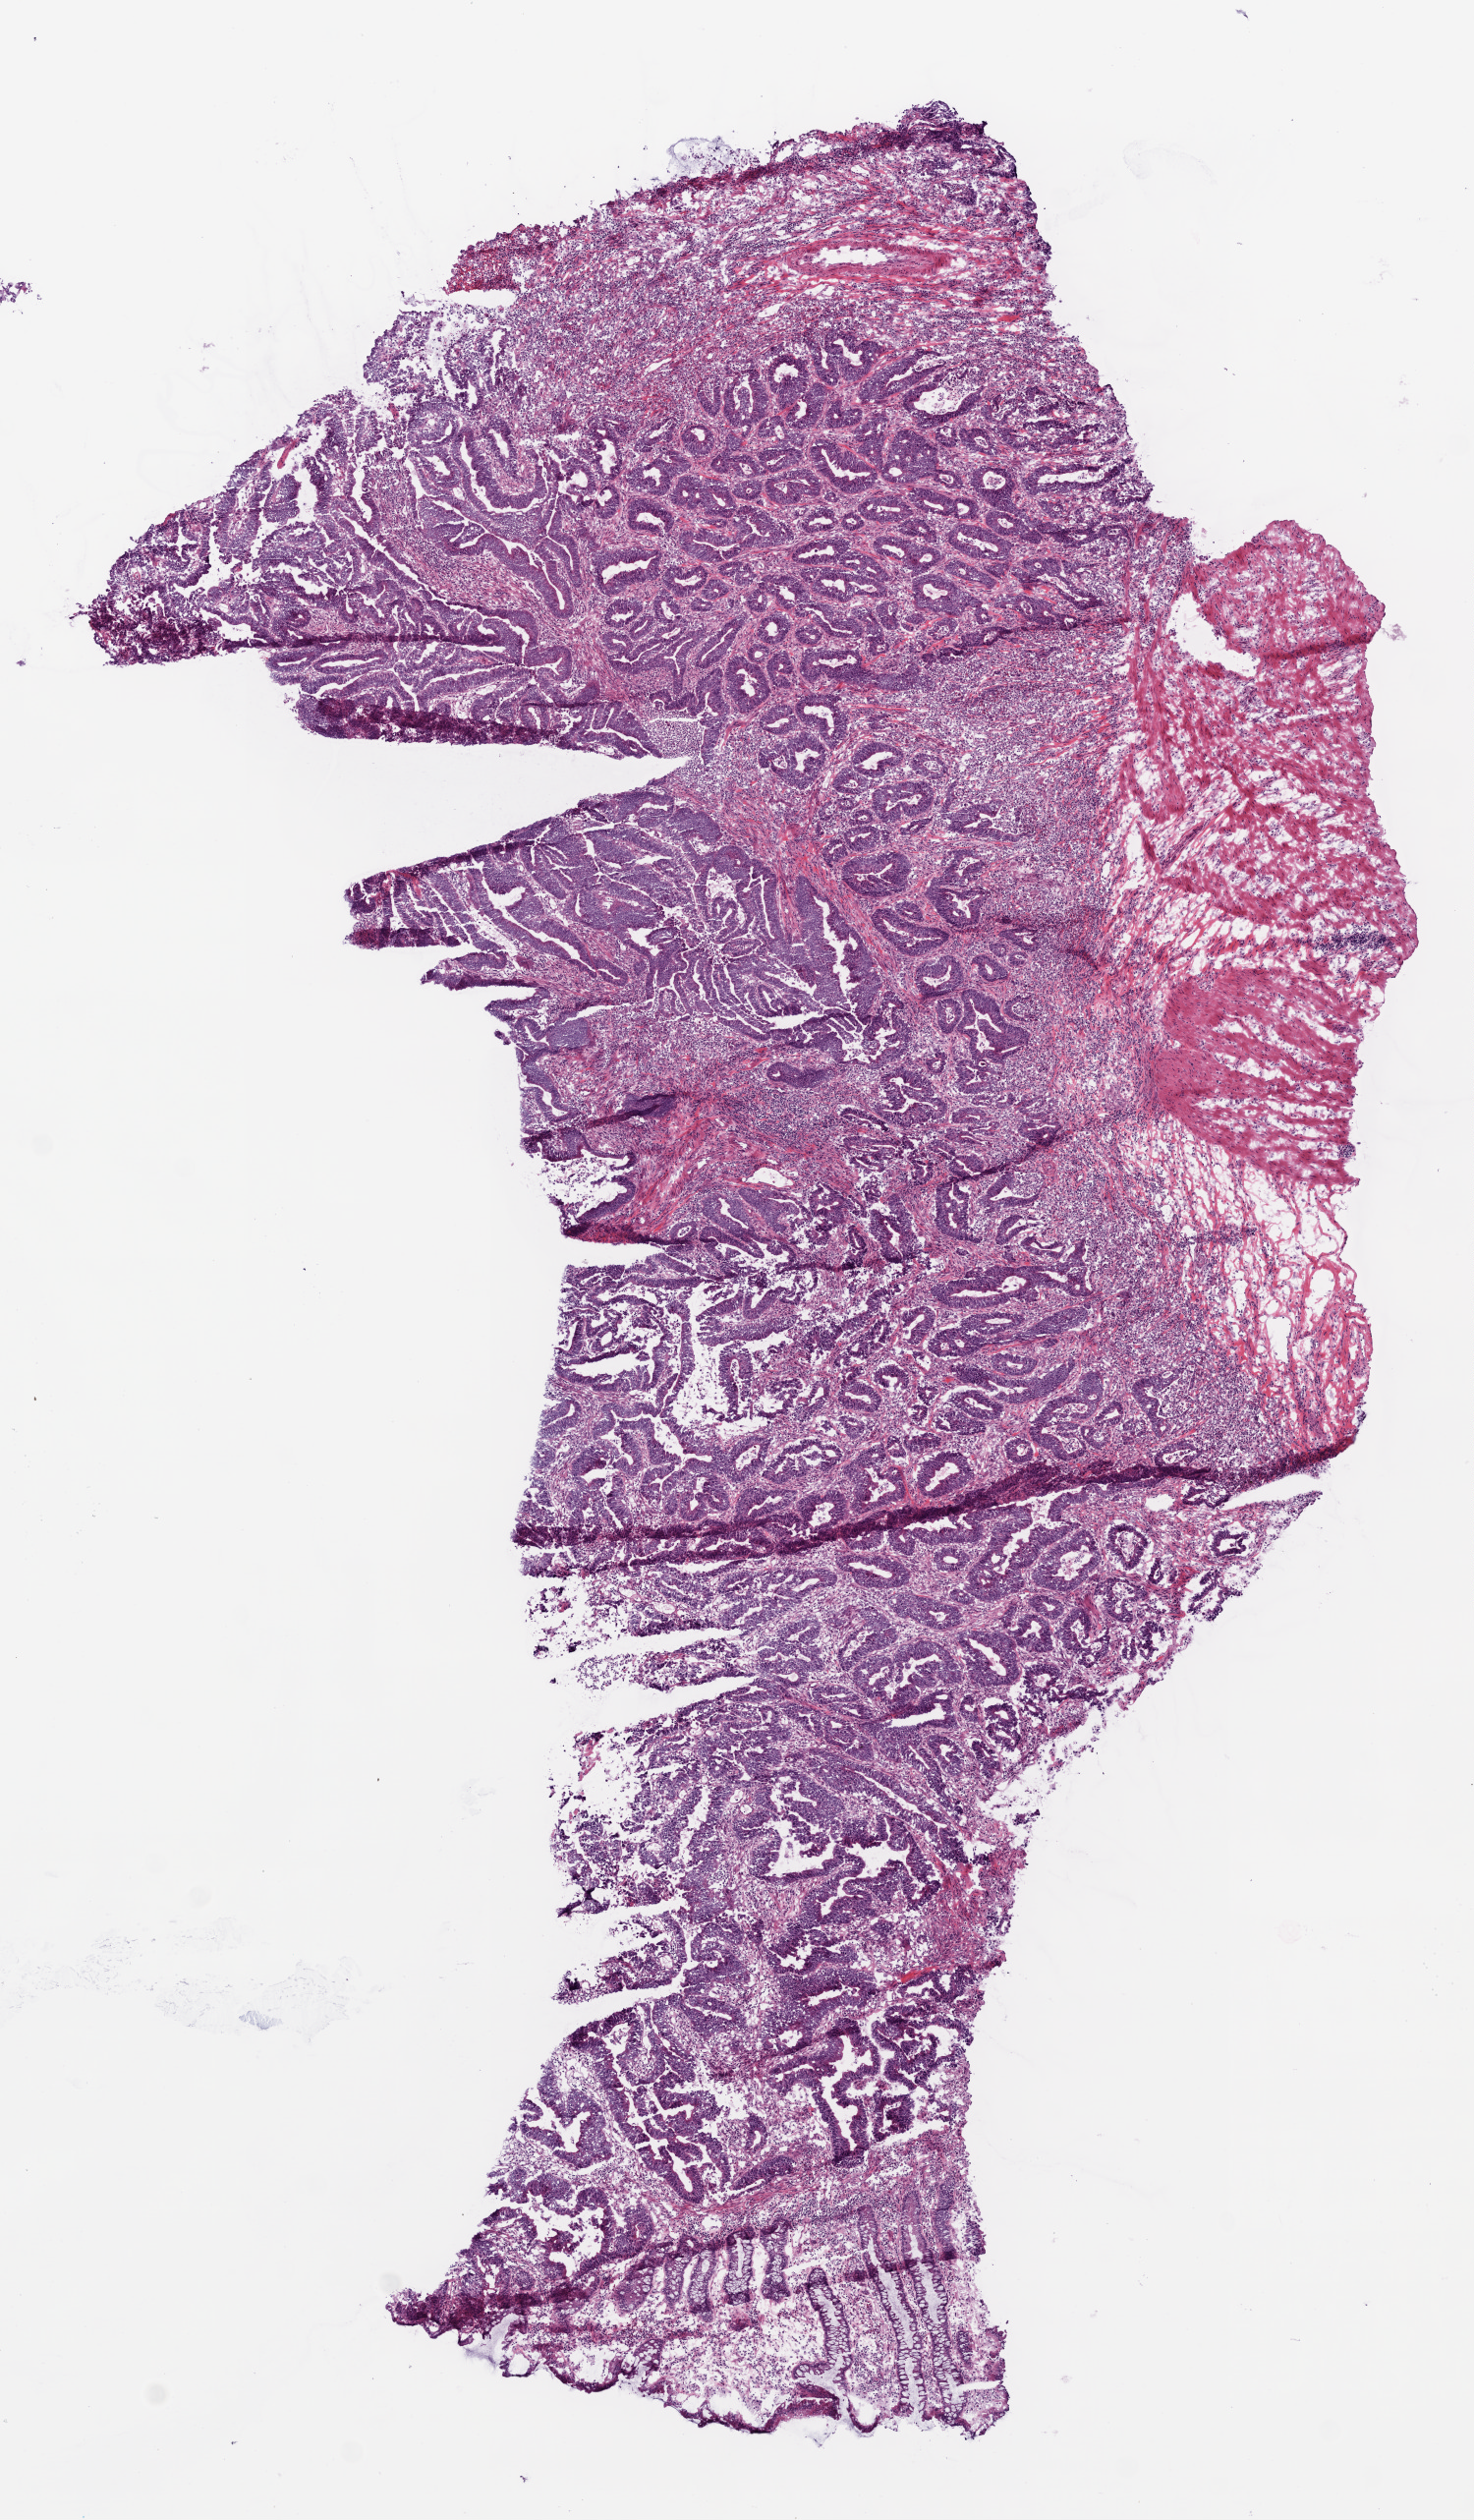
Digitized Hematoxylin and eosin (H&E) stained tissue section (whole slide), a low-resolution overview of the entire scanned area, about 6.0 x 10.3 mm (from a 20x scan); frozen section; primary tumour sample from the colon. Female patient; age at initial diagnosis 61 years. Composition of this section per pathologist review: tumour cells 80%, tumour nuclei 70%, normal cells 5%, stromal cells 15%, necrosis 0%. Infiltration values recorded for this section: lymphocyte infiltration 16%, neutrophil infiltration 3%.
• AJCC pathologic stage: IIA
• lymph nodes positive (case pathology): 0 of 12 examined
• diagnosis: Adenocarcinoma, NOS (sigmoid colon)